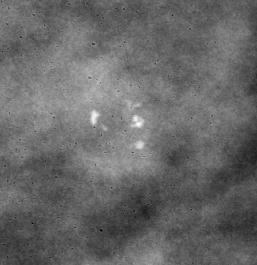
Cropped region of a digitized screen-film mammogram centred on a radiologist-marked abnormality, right breast, CC view, BI-RADS breast density category 3 (scale 1–4).
Marked abnormality: calcifications, morphology pleomorphic, distribution clustered; BI-RADS assessment category 4; pathology result (as recorded, not read from the image): benign.